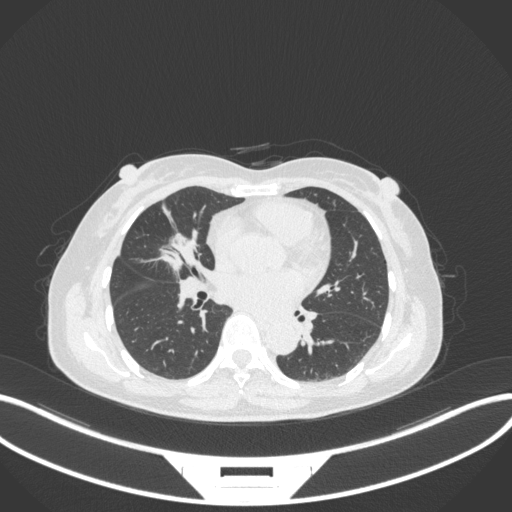
Chest CT, one axial slice. Position 145 of 282 along the scan axis. Reconstruction kernel B31f. 120 kVp. Lung window (W 1500 / L -600 HU). 1 mm slice thickness. 512 × 512 image matrix, field of view 400 × 400 mm. Patient: female, 51 years. Case-level facts recorded for this patient, not image findings: clinical TNM (as recorded): T1c N0 M0; histopathological grade: G2.
Structures marked on this image (bounding box drawn by a radiologist):
- lung tumour (recorded histology: adenocarcinoma): bounding box <157,230,200,270> (left, top, right, bottom; pixels)